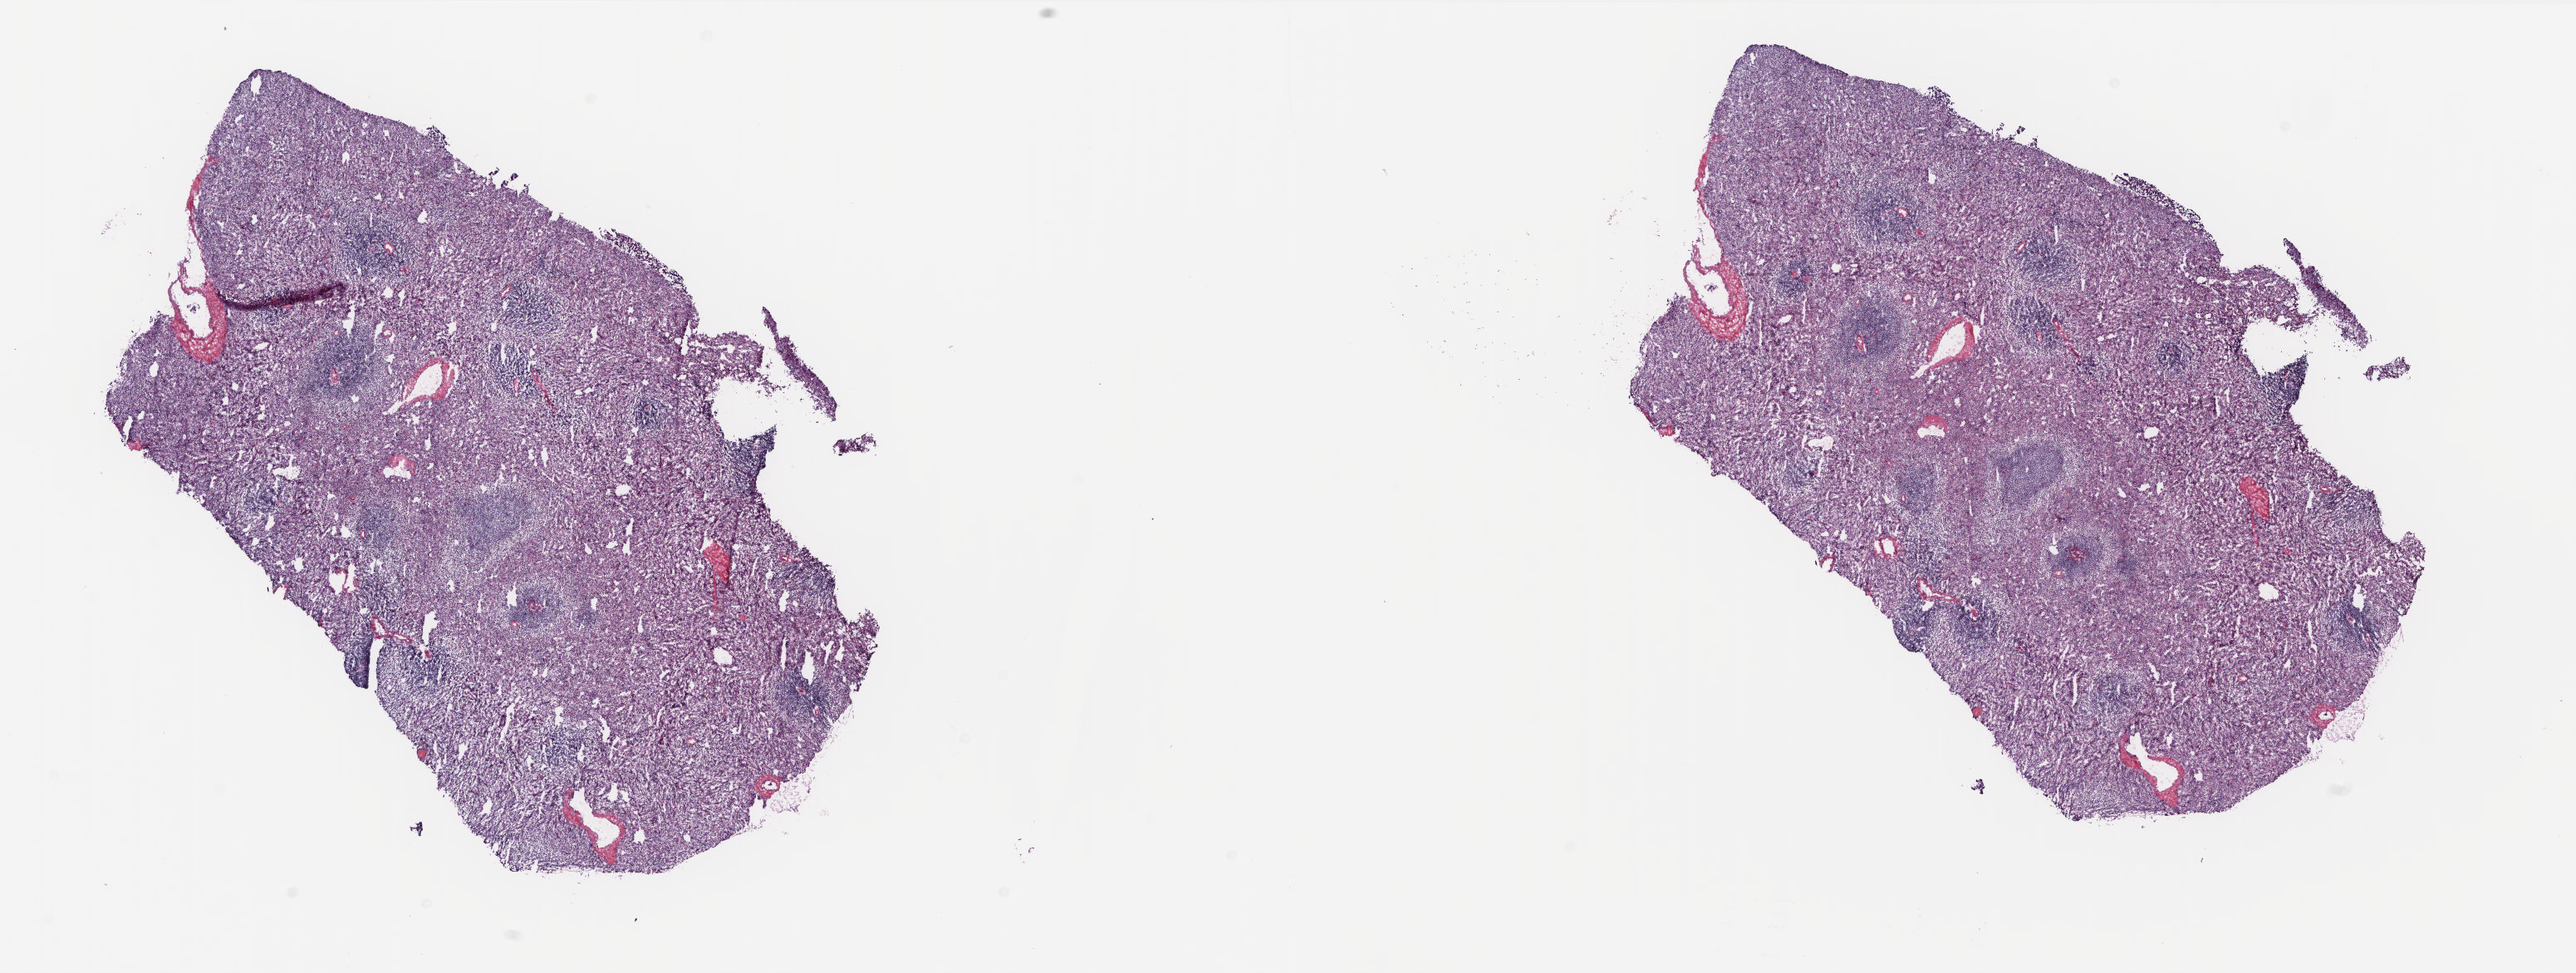
Digitized H&E-stained tissue section (whole slide), low-resolution overview of the scanned area, about 25.0 x 9.4 mm, frozen section, solid tissue normal (non-tumour tissue) sample from the adrenal gland. Female, age 35 years at initial diagnosis. Pathologist review of this section (percent, as recorded): tumour cells 0%, tumour nuclei 0%, normal cells 100%, stromal cells 0%, necrosis 0%. Inflammatory infiltration, as recorded: lymphocyte infiltration 0%, monocyte infiltration 0%, neutrophil infiltration 0%.
This section: solid tissue normal sample (biorepository sample class). Patient diagnosis: Carcinoid tumor, NOS (pancreas, NOS).